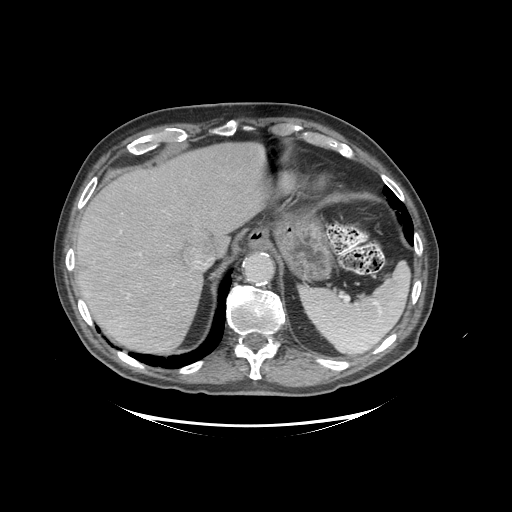
Contrast-enhanced abdominal CT (liver protocol), one axial slice; position 77 of 99 along the scan axis; reconstruction kernel STANDARD; 140 kVp; soft-tissue window (W 400 / L 40 HU); 512 × 512 image matrix, field of view 460 × 460 mm. Case-level facts recorded for this patient, not image findings: diagnosis: hepatocellular carcinoma (patient treated with transarterial chemoembolisation; whether this scan precedes or follows treatment is not stated here); TNM stage (as recorded): Stage-I; Child-Pugh class: A; tumour differentiation: moderately differentiated; tumour nodularity: uninodular.
Annotated regions visible in this slice (semi-automatically segmented with operator editing):
- liver parenchyma outside the tumour (the mass and vessels are separate outlines, so this box may not span the whole liver): bounding box <74,142,268,352> (left, top, right, bottom; pixels)
- liver vessels: <198,261,200,263>